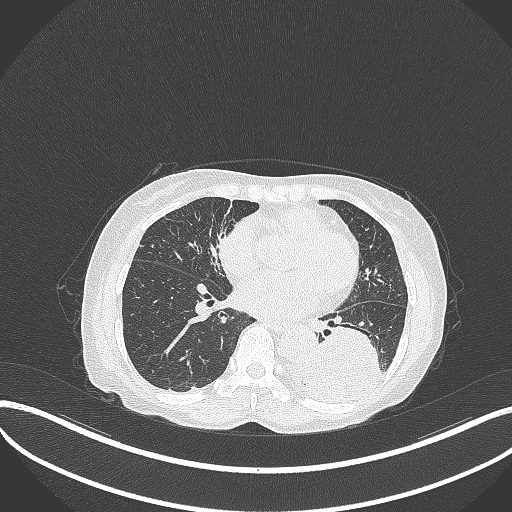
Chest CT, one axial slice. Position 130 of 370 along the scan axis. Lung window (W 1500 / L -600 HU). 512 × 512 image matrix, field of view 400 × 400 mm. Female patient, age 78 years. Case-level facts recorded for this patient, not image findings: clinical TNM (as recorded): T3 N0 M1.
Outlined on this slice (bounding box drawn by a radiologist):
- lung tumour (recorded histology: squamous cell carcinoma): bounding box (x1, y1, x2, y2) in pixels: (302, 318, 389, 400)